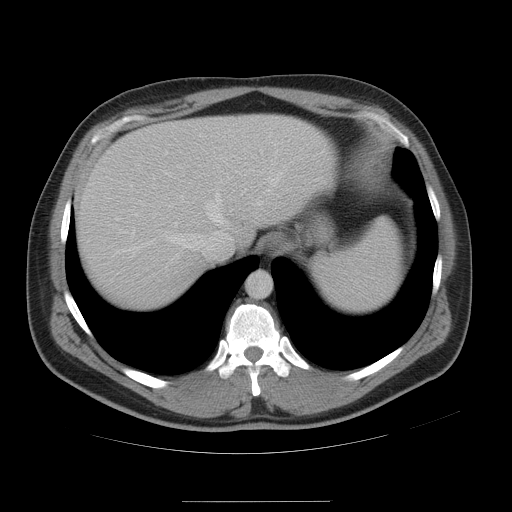
Contrast-enhanced abdominal CT, one axial slice; slice 42 of 54 in the series (ordered by position); intravenous contrast given; soft-tissue window (W 400 / L 40 HU); 5 mm slice thickness; 512 × 512 image matrix. Male patient, age 40 years. Case-level facts recorded for this patient, not image findings: diagnosis: colorectal cancer liver metastases, imaged before liver resection; multiple liver metastases: no; largest metastasis: 15 cm; disease in both lobes: no.
Outlined on this slice (expert manual segmentation):
- hepatic veins: bounding box (x1, y1, x2, y2) in pixels: (119, 171, 283, 254)
- liver: (76, 115, 339, 312)
- planned liver remnant (the part of the liver to remain after resection): (166, 115, 339, 268)